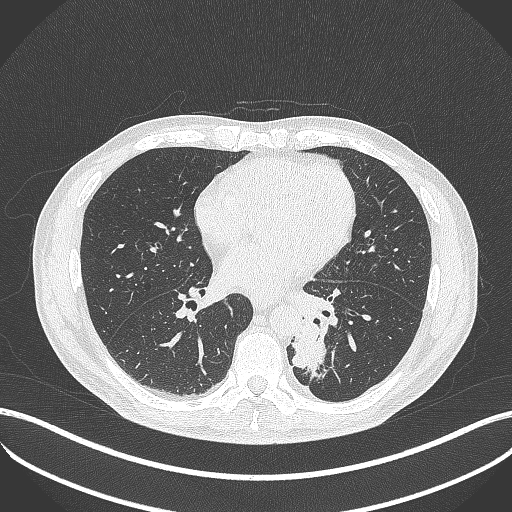
Chest CT, one axial slice. Slice 175 of 451 in the series (ordered by position). Reconstruction kernel B70f. Lung window (W 1500 / L -600 HU). 512 × 512 image matrix. Patient: male, 72 years. From the clinical record (not read from this slice): clinical TNM (as recorded): T2b N0 M1.
Annotated regions visible in this slice (bounding box drawn by a radiologist):
- lung tumour (recorded histology: adenocarcinoma): bounding box <290,315,328,376> (left, top, right, bottom; pixels)